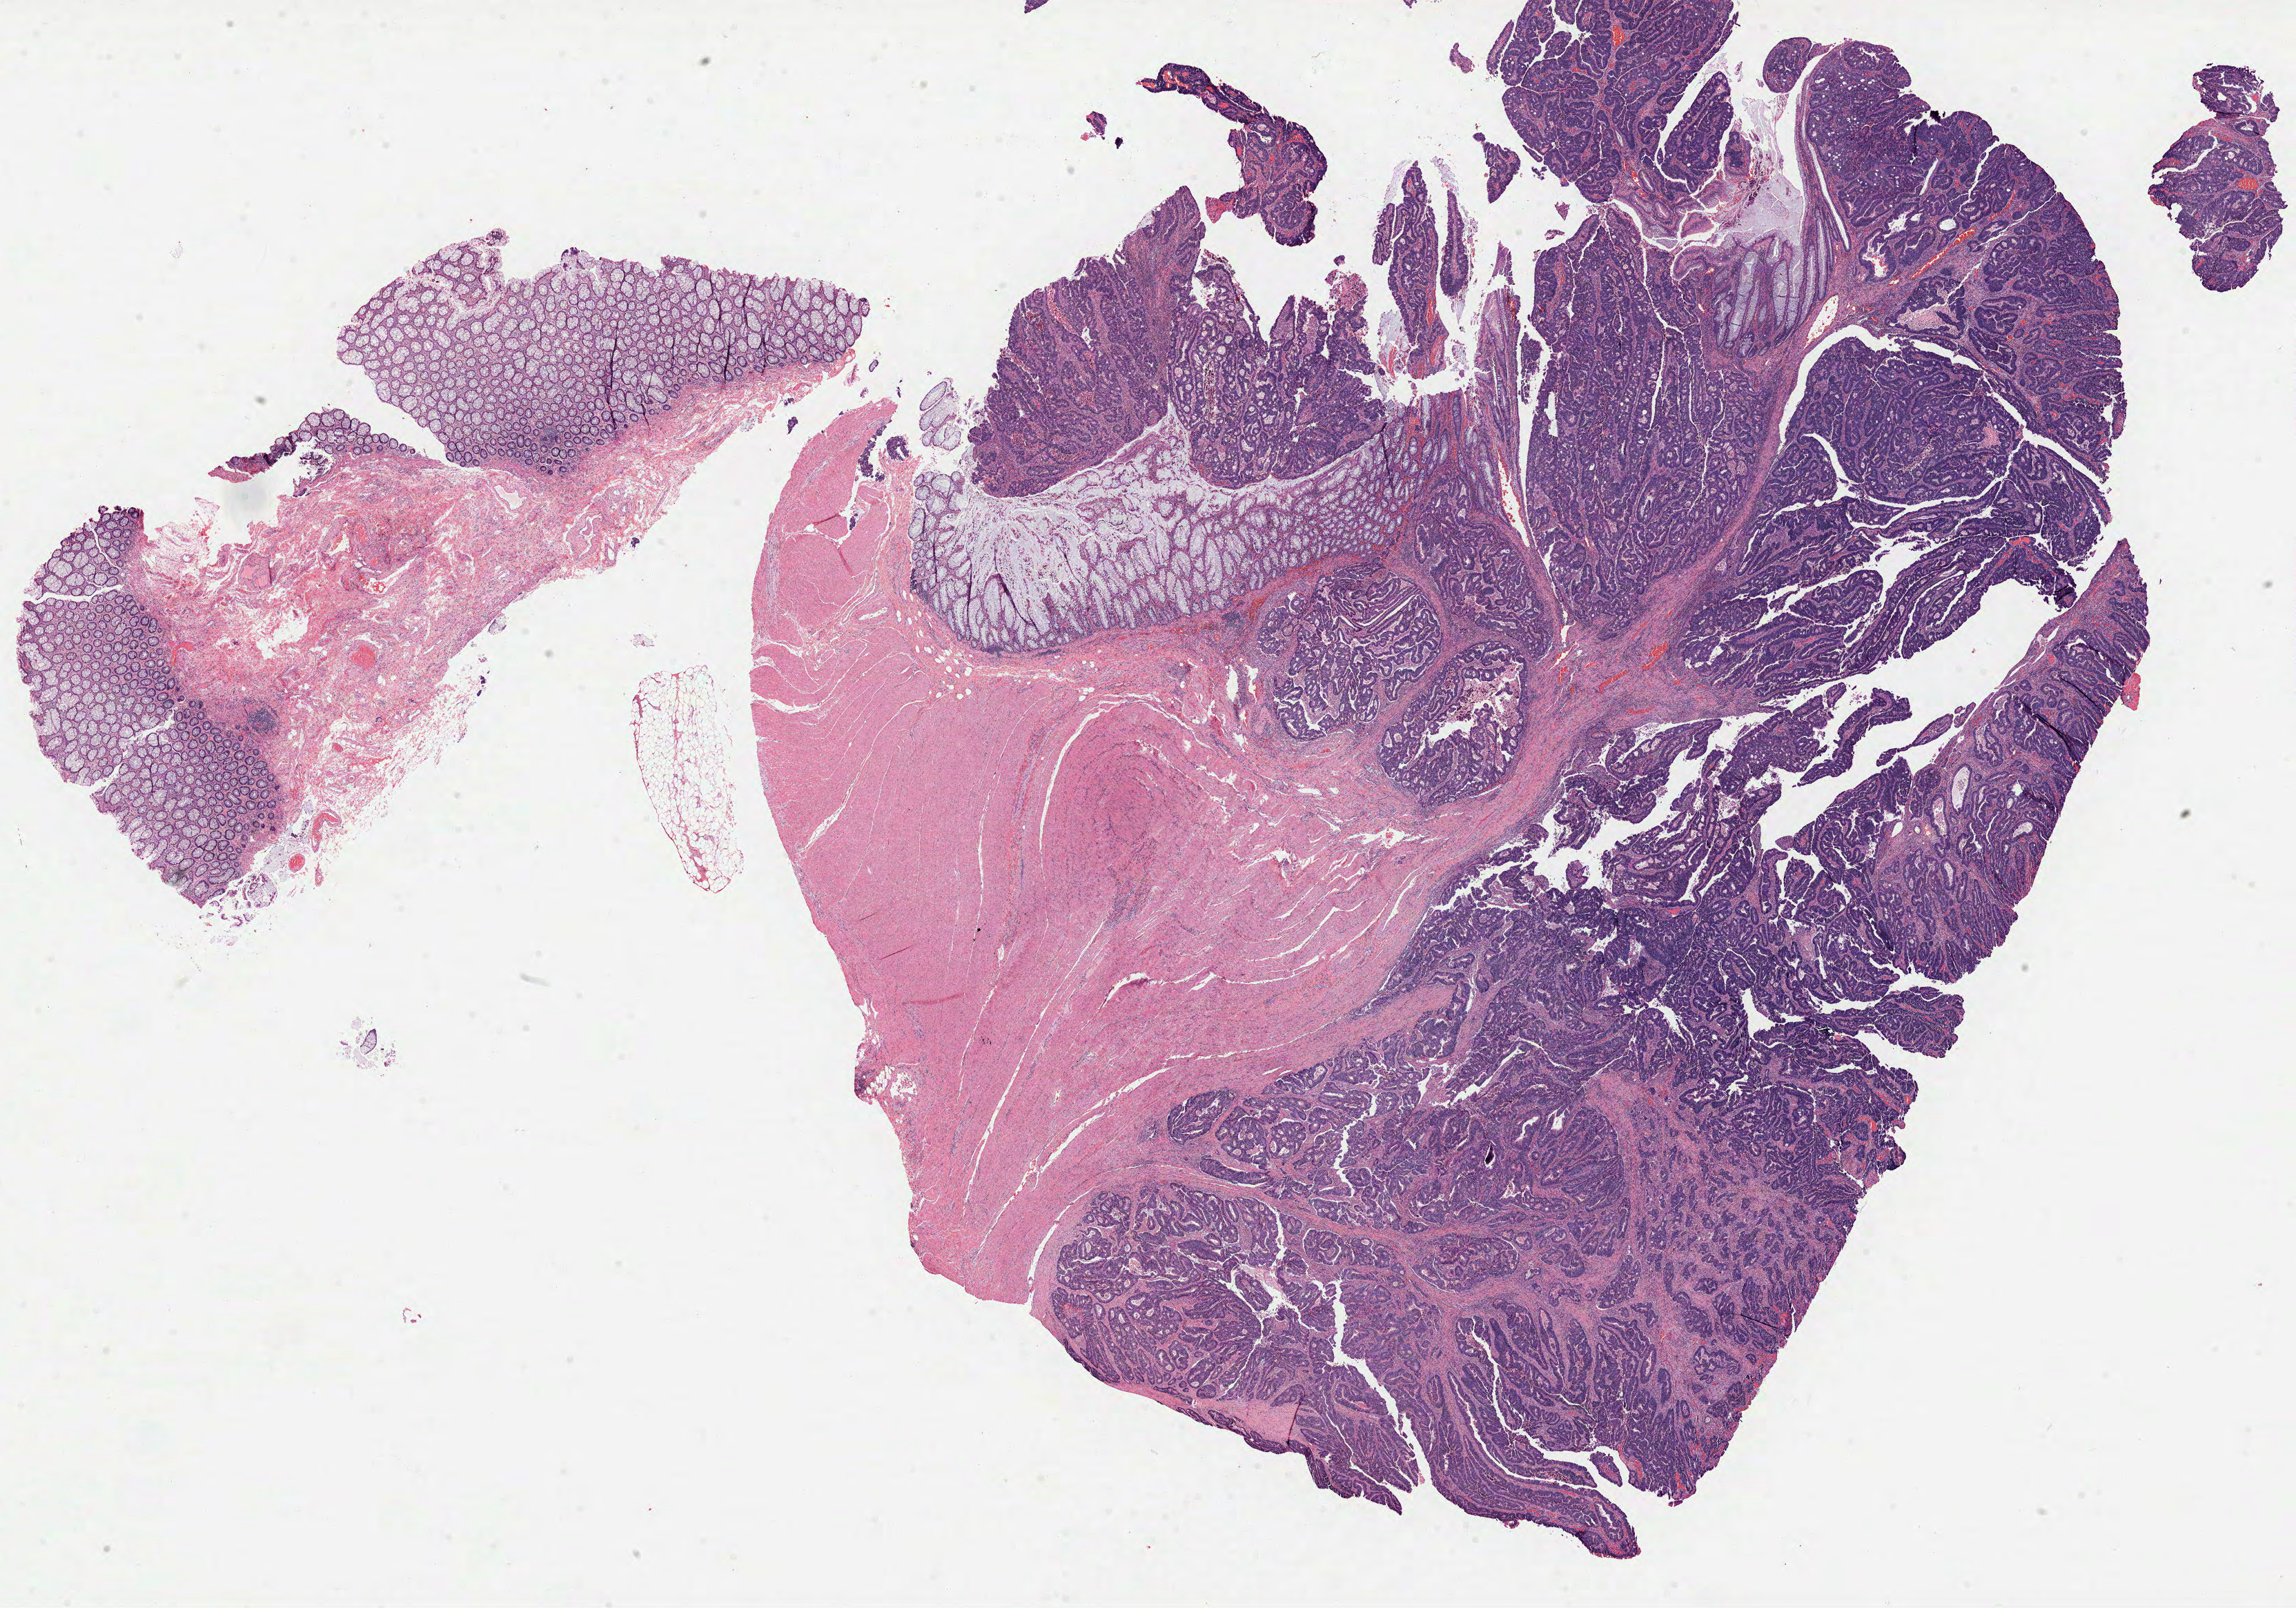
Hematoxylin and eosin (H&E) stained whole-slide image — a low-resolution overview of the entire scanned area, about 26.8 x 18.8 mm (acquisition: 40x scan); formalin-fixed paraffin-embedded (FFPE) diagnostic section; primary tumour sample from the colon. Male patient; age at initial diagnosis 81 years.
* TNM: T3 N1 MX
* AJCC pathologic stage: IIIB (6th edition)
* diagnosis: Adenocarcinoma, NOS (sigmoid colon)